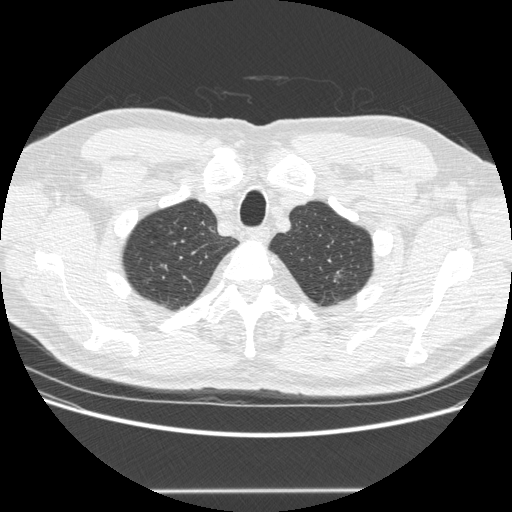
Axial slice from a low-dose chest CT screening exam, second screening round (one year after baseline), lung window (W 1500 / L -600 HU), 1.25 mm slice thickness, 120 kVp, slice 47 of 223 in the series, 512 × 512 image matrix. Male, age 69 years at enrolment.
• Lesion marked by an expert reader, bounding box [x1, y1, x2, y2] px = [312, 262, 347, 293].
• Screening reader's record for this exam: no non-calcified nodule ≥4 mm recorded.